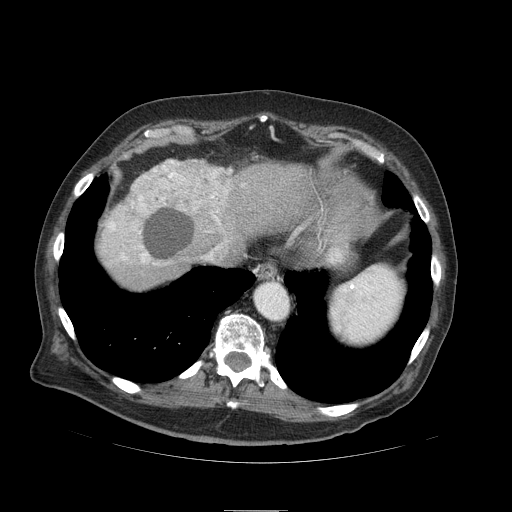
Contrast-enhanced abdominal CT (liver protocol), one axial slice; slice 78 of 103 in the series (ordered by position); 120 kVp; soft-tissue window (W 400 / L 40 HU); 2.5 mm slice thickness; 512 × 512 image matrix. Case-level facts recorded for this patient, not image findings: diagnosis: hepatocellular carcinoma (patient treated with transarterial chemoembolisation; whether this scan precedes or follows treatment is not stated here); TNM stage (as recorded): Stage-IIIA; Child-Pugh class: B; tumour differentiation: well differentiated; tumour nodularity: multinodular.
Annotated regions visible in this slice (semi-automatic segmentation, software-assisted and operator-edited):
- abdominal aorta: box from (x=255, y=282) to (x=288, y=319) px
- liver parenchyma outside the tumour (the mass and vessels are separate outlines, so this box may not span the whole liver): (x=97, y=160)–(x=314, y=290)
- mass: (x=99, y=158)–(x=233, y=267)
- liver vessels: (x=217, y=219)–(x=219, y=221)